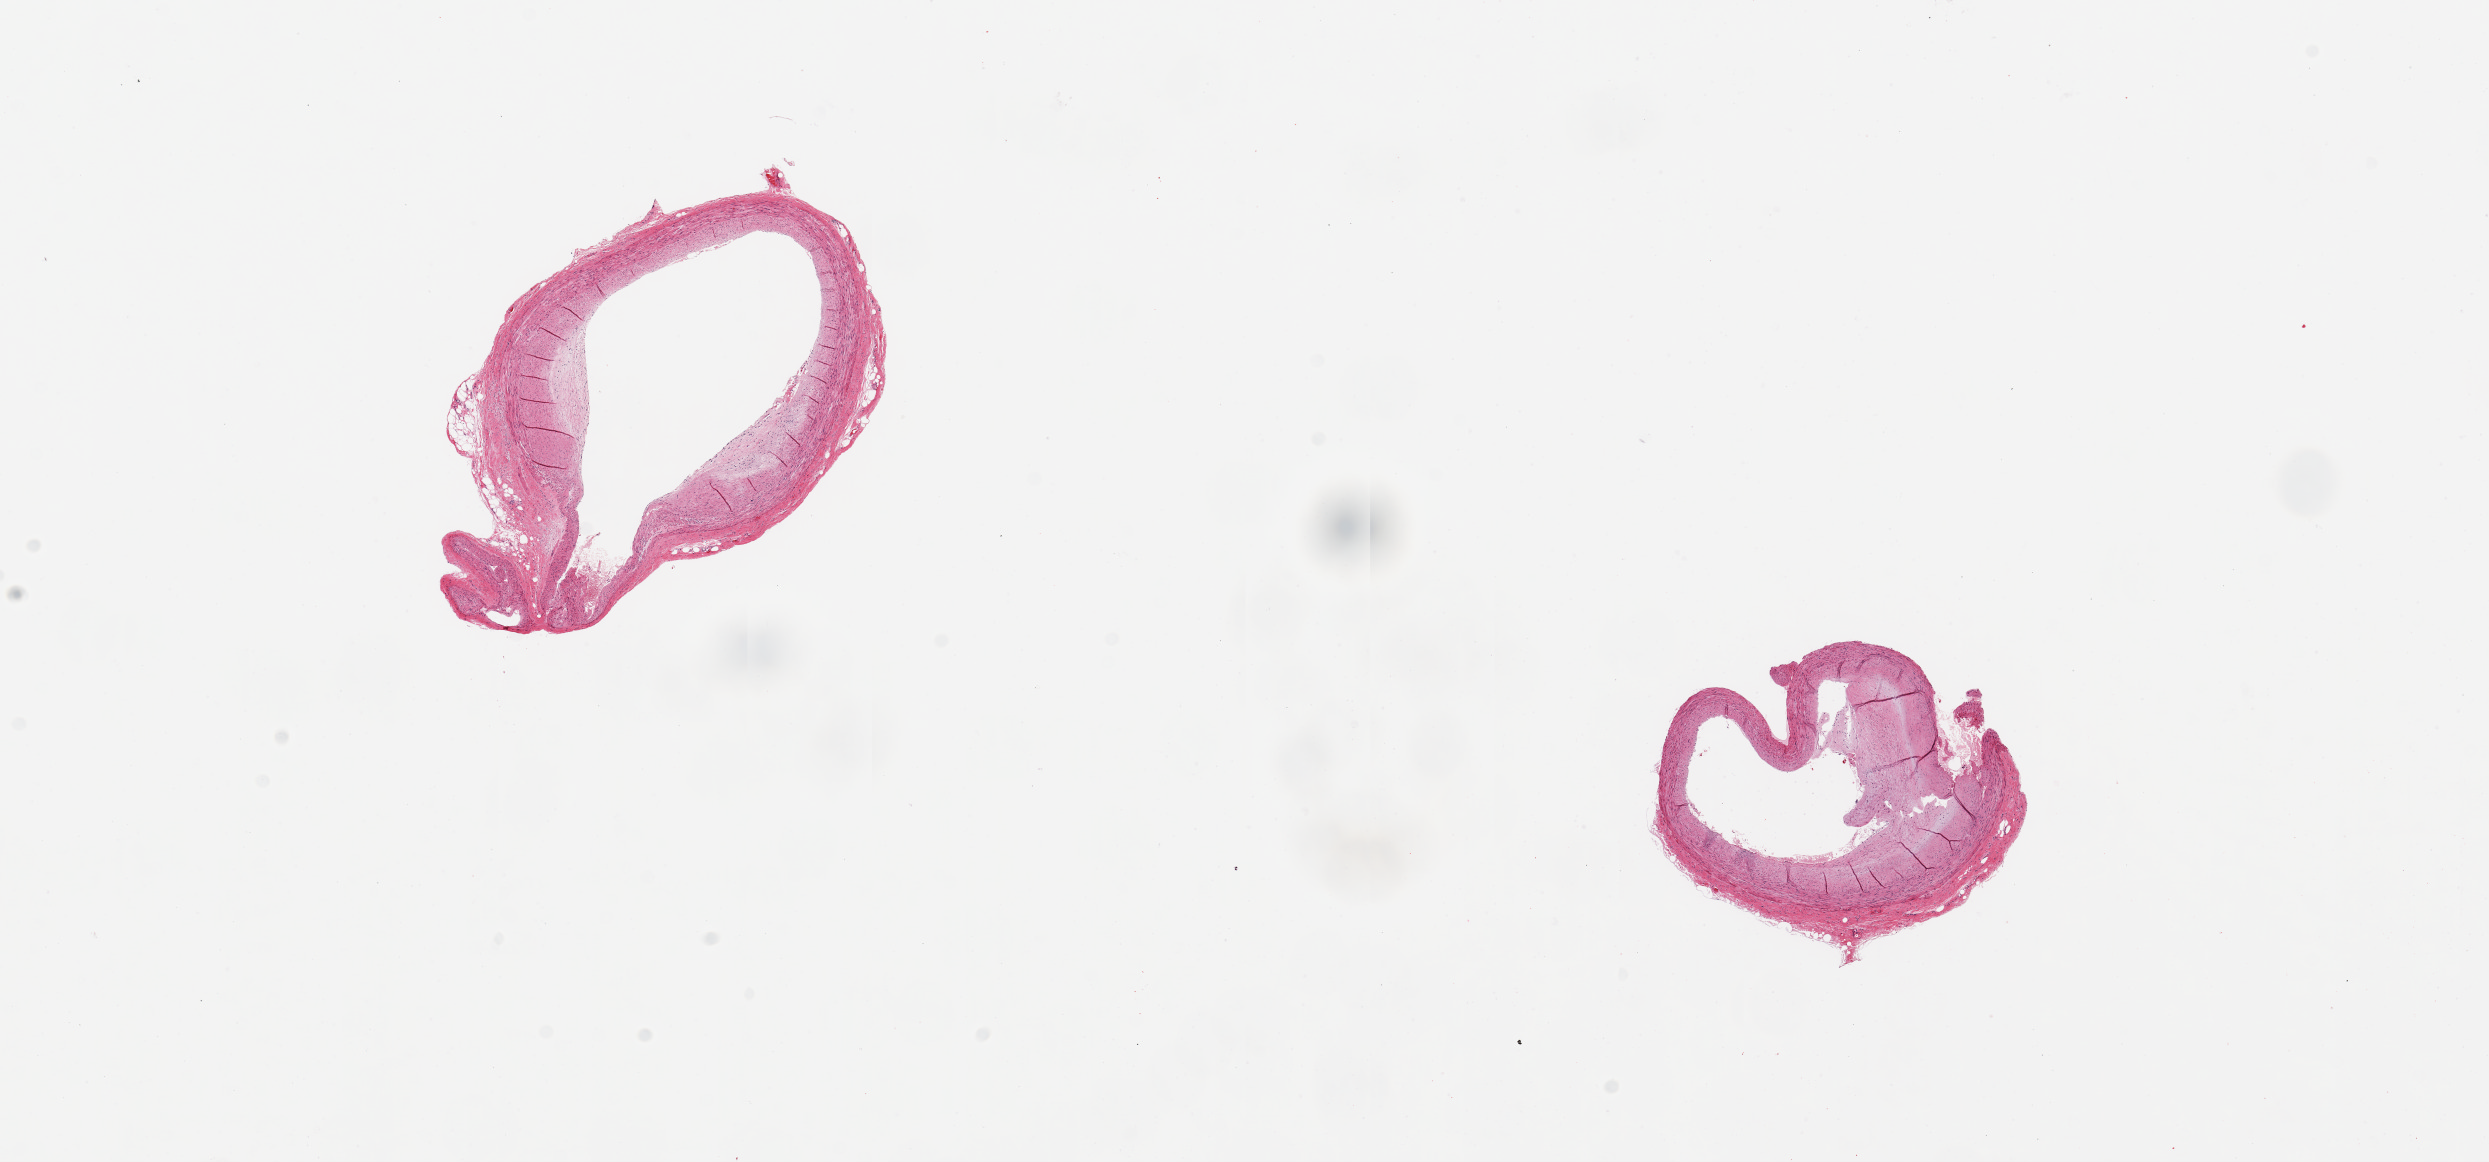
Whole-slide image, hematoxylin and eosin (H&E) stain, brightfield — low-resolution overview of the scanned area, about 19.7 x 9.2 mm (from a 20x scan); PAXgene-fixed paraffin-embedded (PFPE) section; target tissue: coronary artery; tissue donor sample. Male donor.
- reviewer comment on this tissue sample: 2 pieces, 4x3 & 3x2.5mm; up to ~30% atherosclerotic occlusion in both